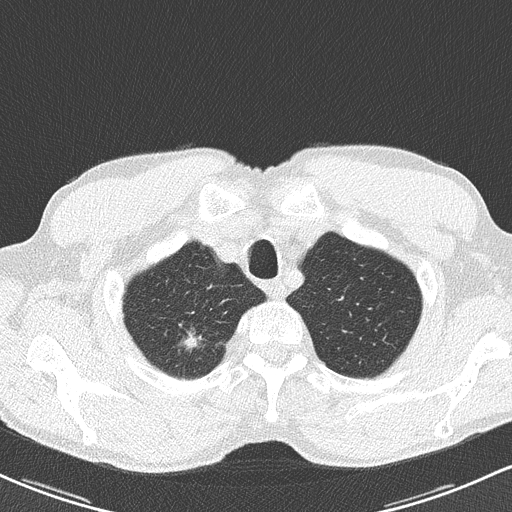
Chest CT (low-dose screening protocol), one axial image, baseline screening round, lung window (W 1500 / L -600 HU), 2 mm slice thickness, lung (sharp) reconstruction kernel (B50f). Male participant, aged 62 years at enrolment. Former smoker at enrolment.
• Expert-annotated lung lesion, bounding box <167,325,214,369> (left, top, right, bottom; pixels).
• Reader record for this screening exam (exam-level; its link to the box is not recorded): non-calcified nodule or mass ≥4 mm, right upper lobe, 12 × 9 mm, spiculated (stellate) margins, soft tissue attenuation.